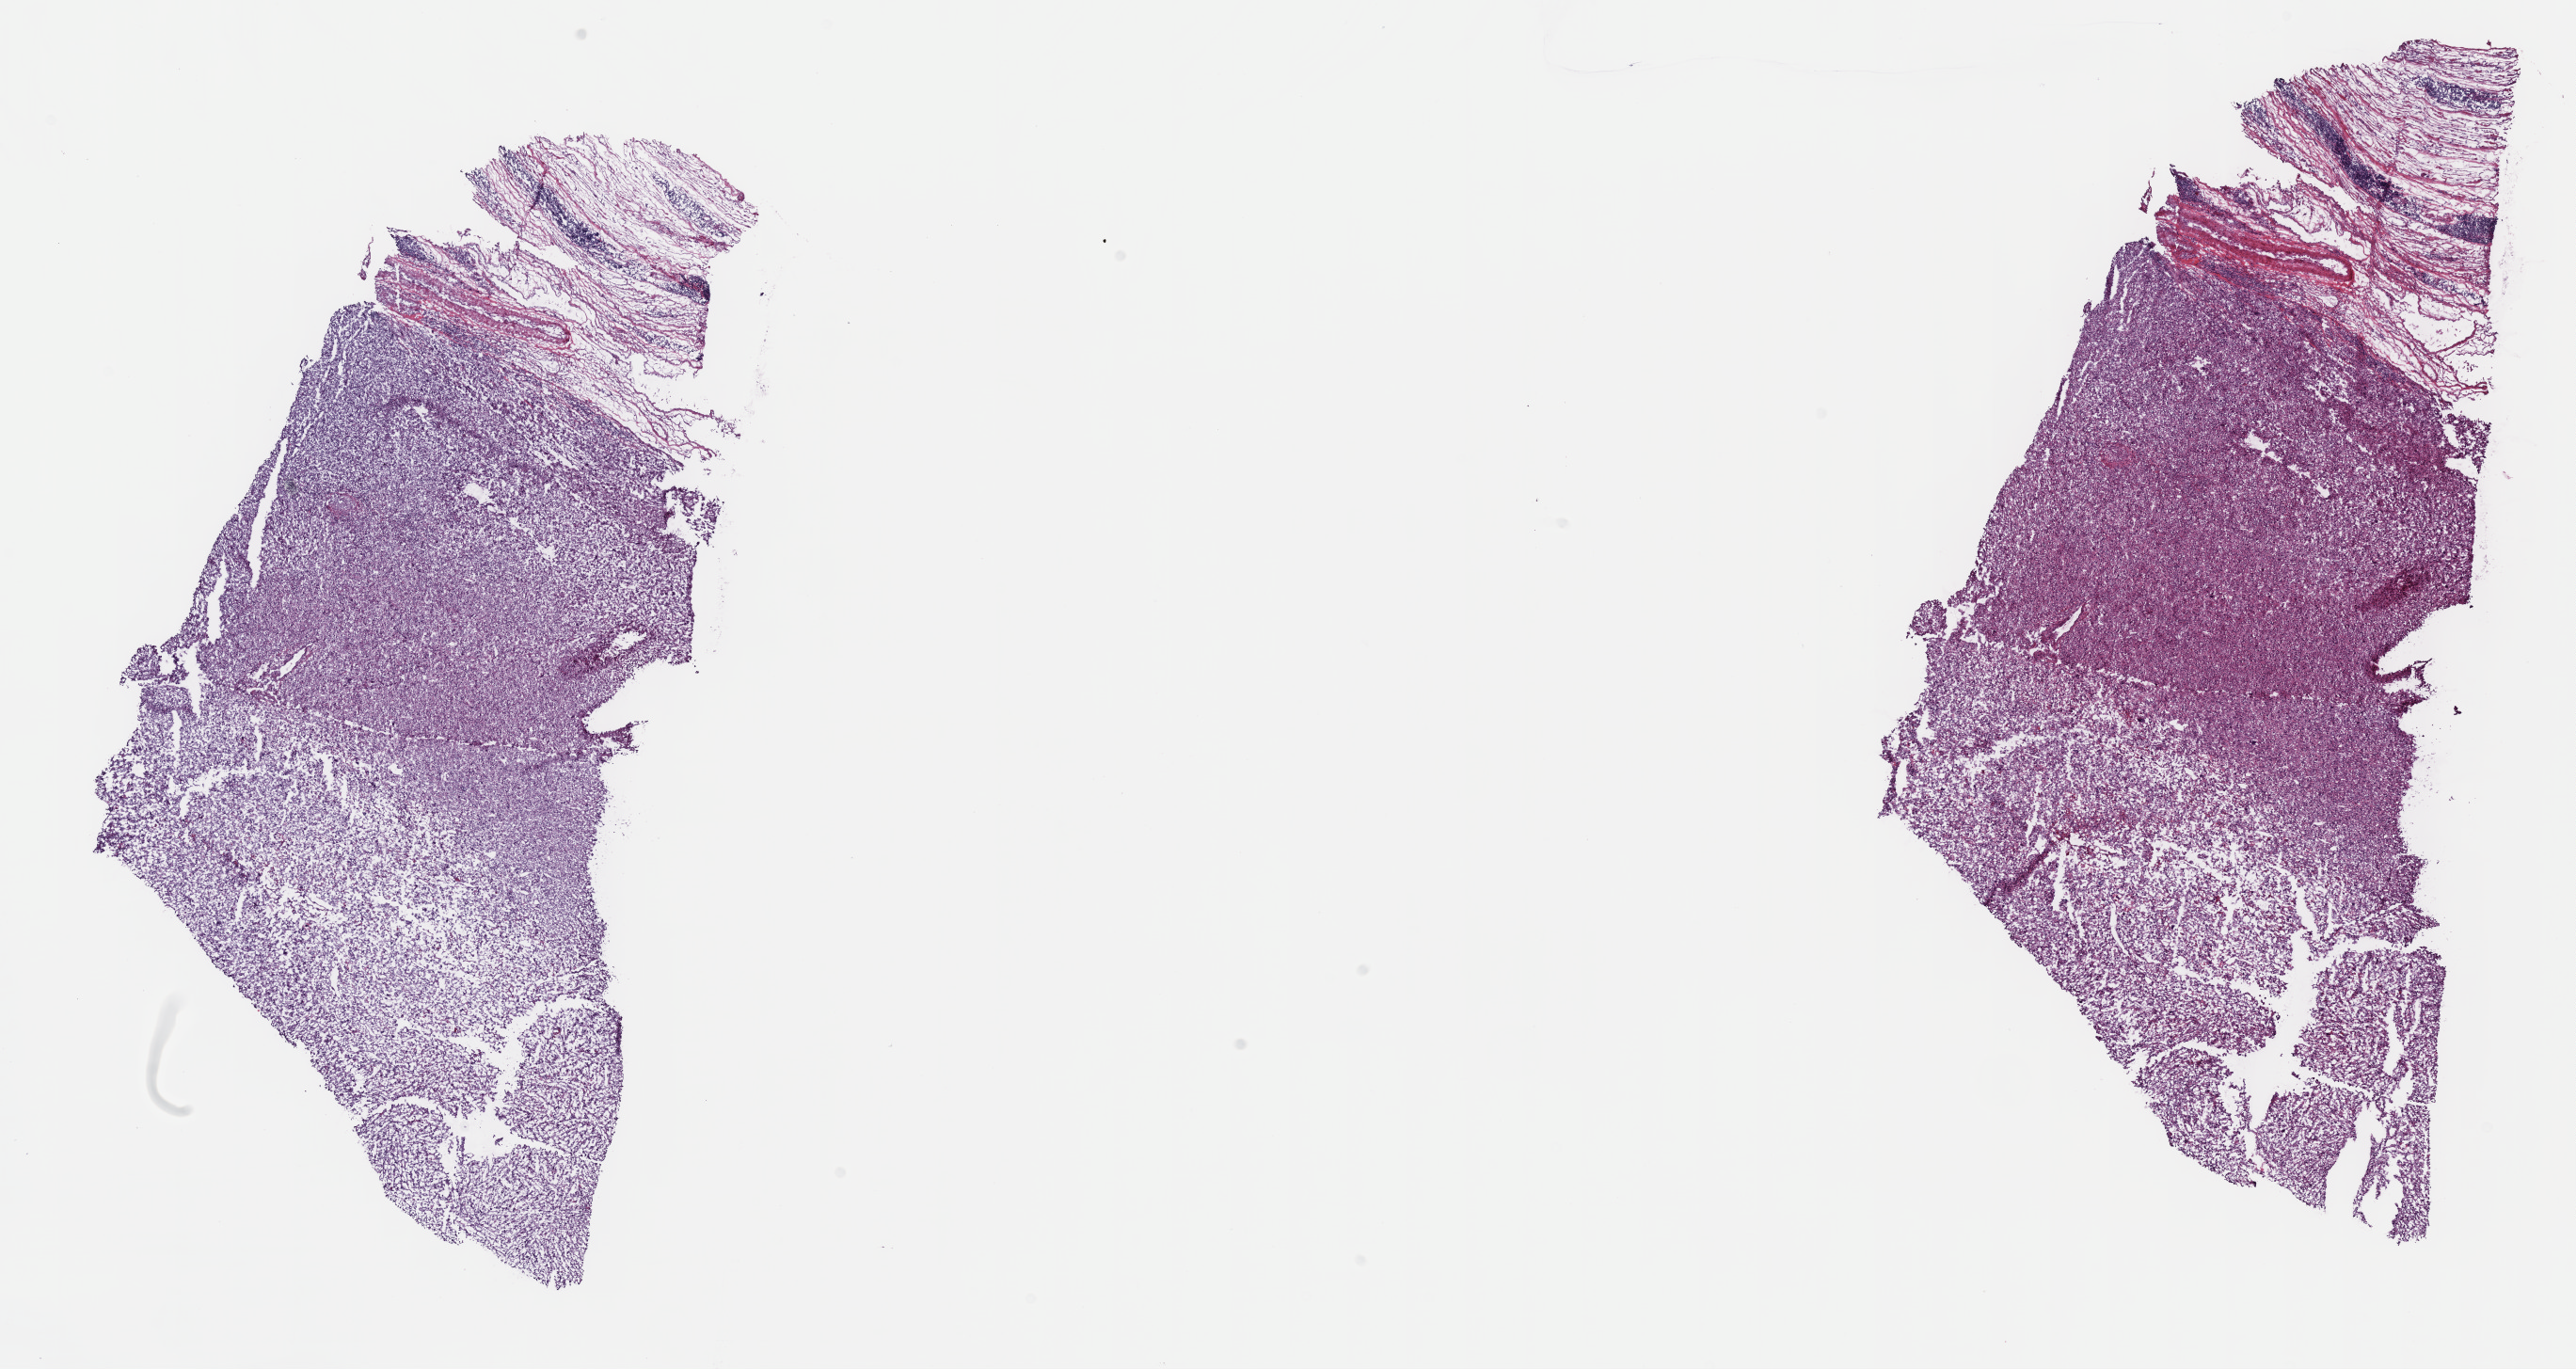
Whole-slide histology image, Hematoxylin and eosin (H&E) stained, whole scanned area (about 22.1 x 11.8 mm, acquisition: 40x scan) shown as a low-resolution overview, frozen section from the top of the tissue portion, primary tumour sample from the connective, subcutaneous and other soft tissues. Patient: female, age at initial diagnosis 62 years. Pathologist review of this section (percent, as recorded): tumour cells 100%, tumour nuclei 80%, normal cells 0%, stromal cells 0%, necrosis 0%. Infiltration values recorded for this section: lymphocyte infiltration 1%, monocyte infiltration 0%, neutrophil infiltration 0%.
• histologic diagnosis: Malignant fibrous histiocytoma